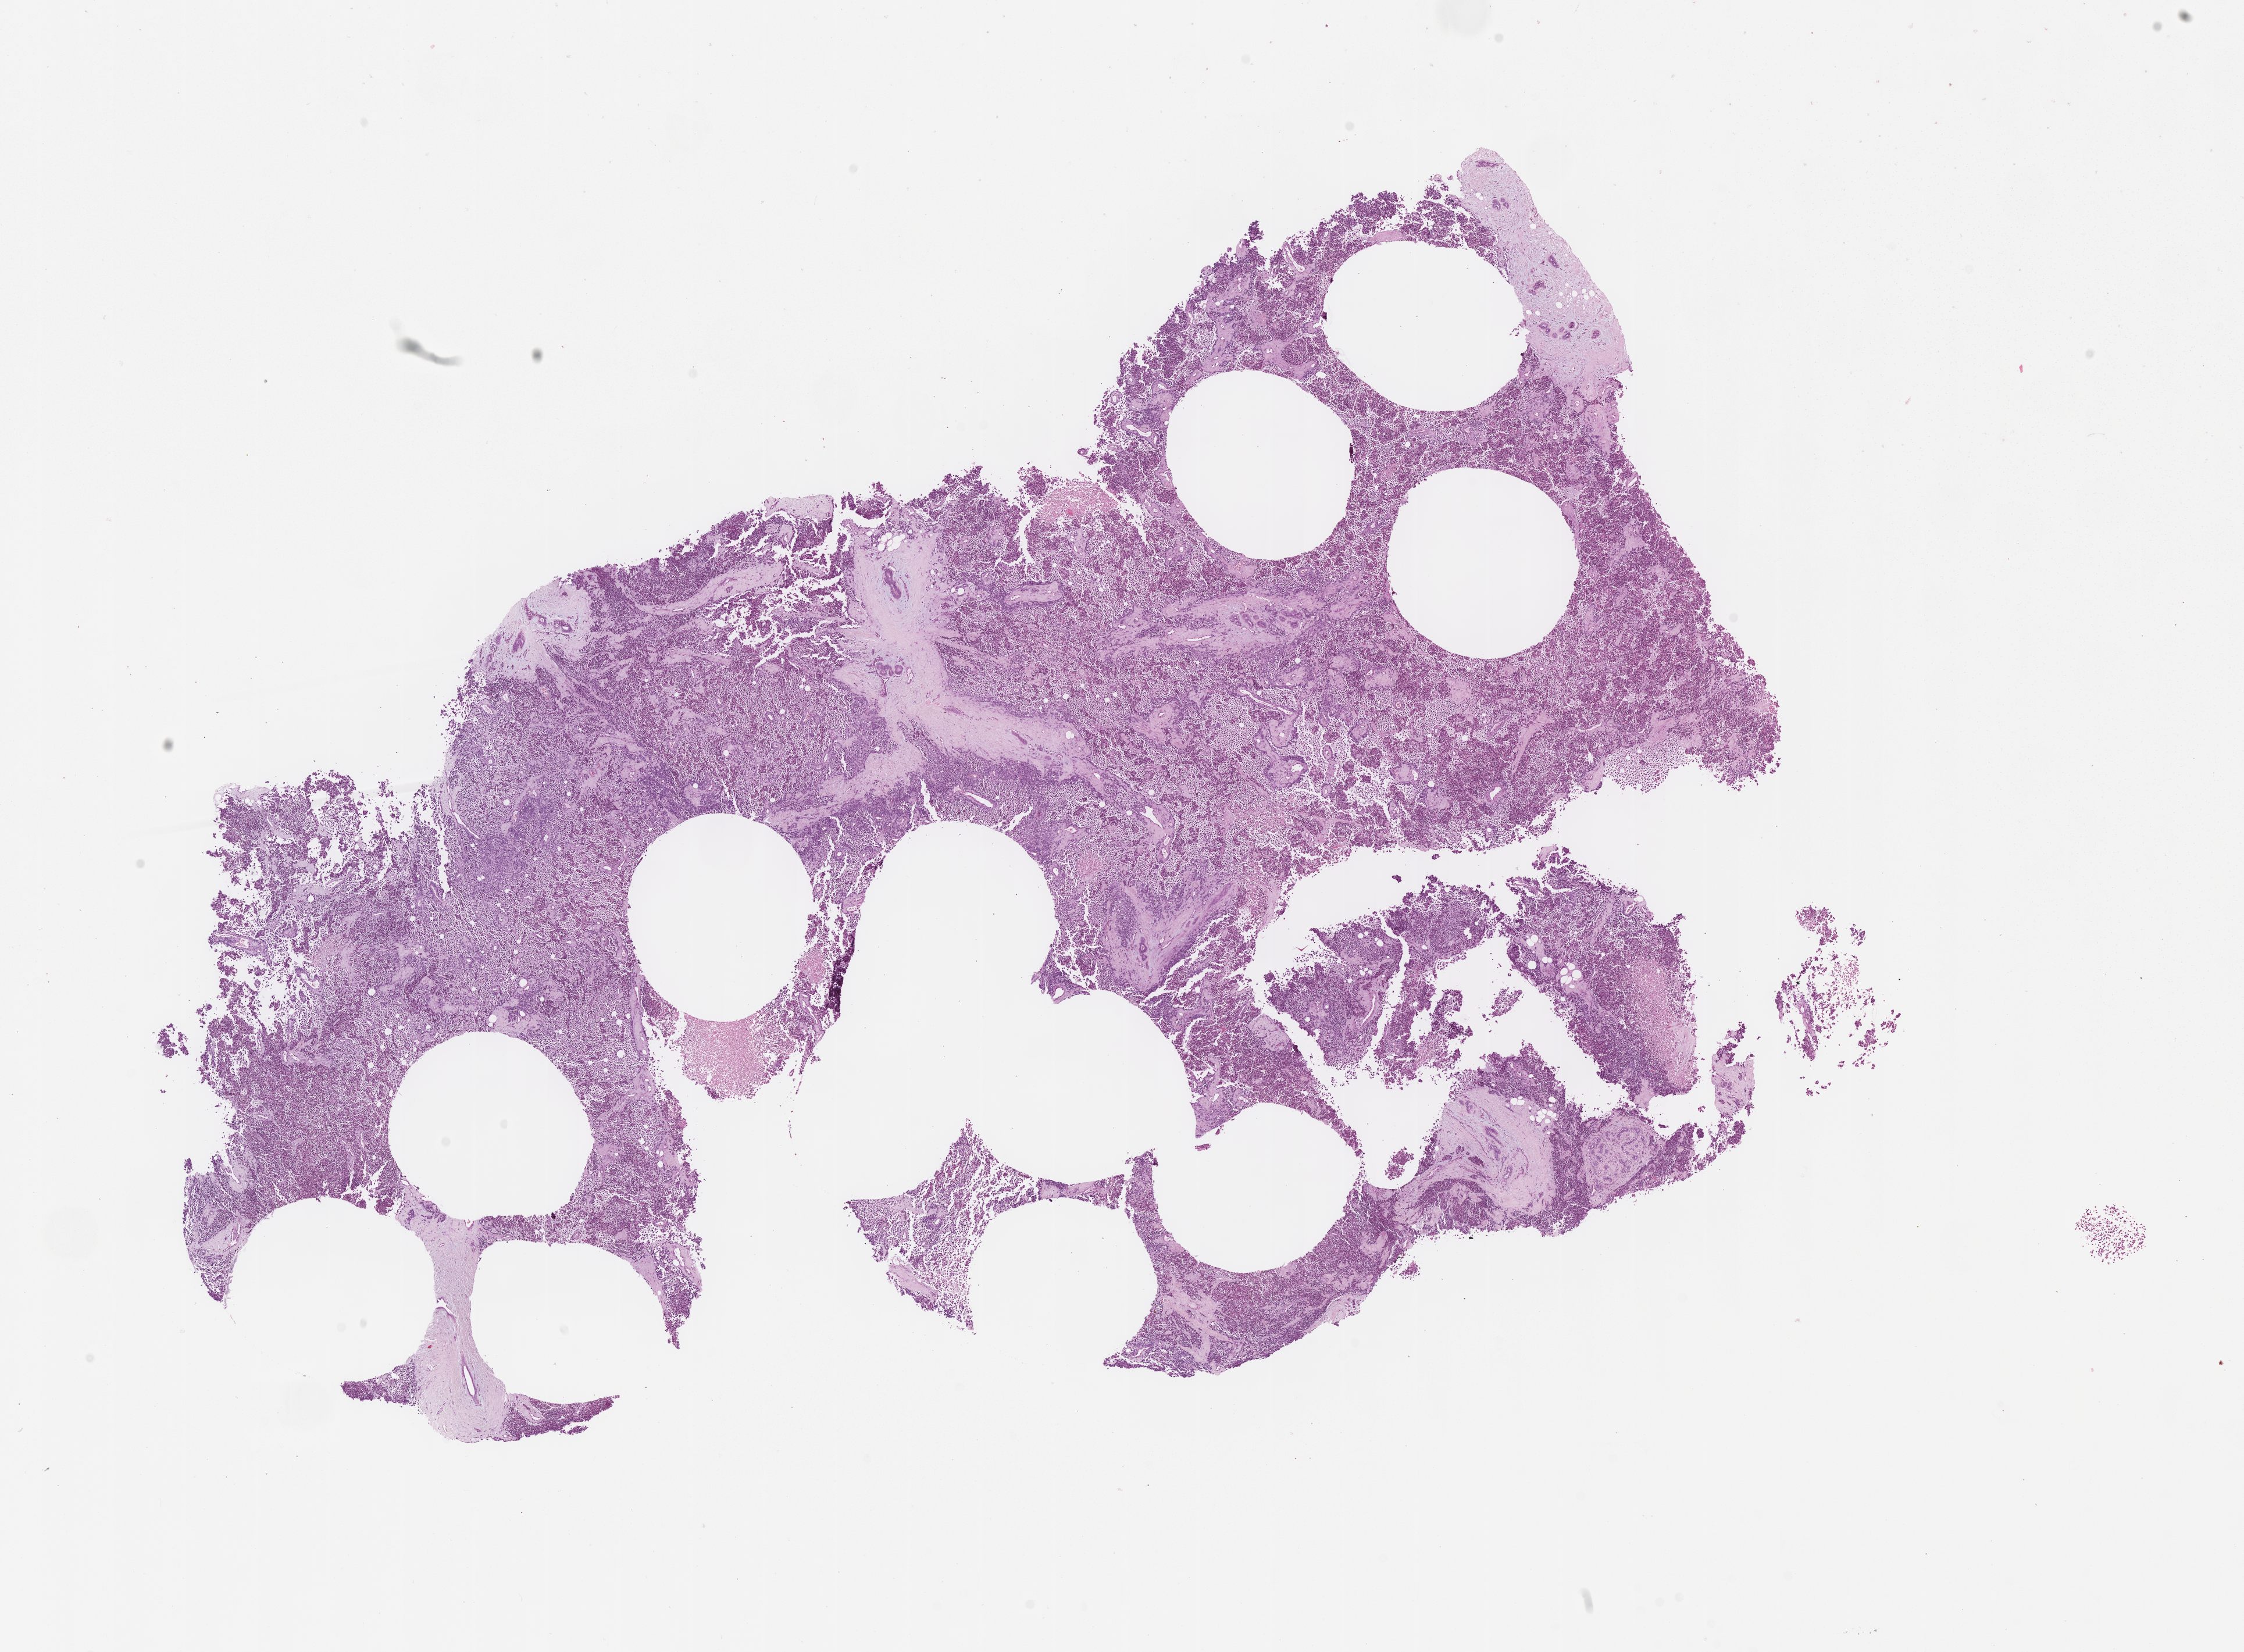
H&E whole-slide image of tumor tissue, low-resolution overview of the scanned area, about 15.6 x 11.5 mm, FFPE section, site: breast-right. Patient: female, age 14.5 years at diagnosis.
Stage (as recorded): 2. Metastatic status at presentation (as recorded): non-metastatic (unconfirmed). Diagnosis: rhabdomyosarcoma; histological classification: alveolar rhabdomyosarcoma.